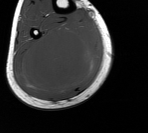
MRI of an extremity soft-tissue mass, one axial slice; slice 58 of 76 in the series (ordered by position); MR volume resampled by the dataset authors to the PET/CT grid (not the native acquisition matrix); 3.27 mm slice thickness; 148 × 133 image matrix, field of view 145 × 130 mm. Male patient. From the clinical record (not read from this slice): histological type: liposarcoma - round cell; grade: high; site of the primary tumour: right calf.
Structures marked on this image (expert contour drawn on MRI and transferred to this co-registered scan by the dataset authors):
- gross tumour volume (mass): bounding box <15,19,103,97> (left, top, right, bottom; pixels)